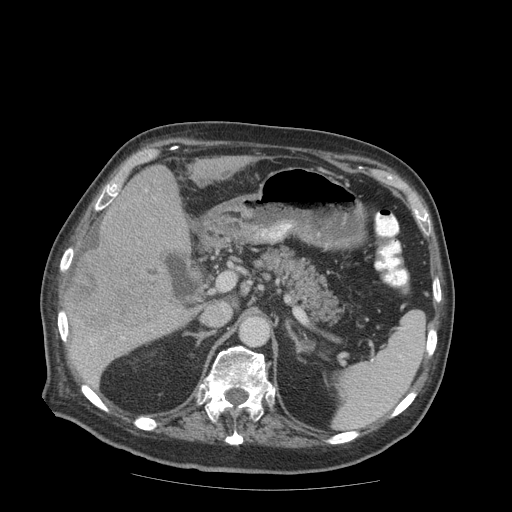
Contrast-enhanced abdominal CT (liver protocol), one axial slice. Position 46 of 99 along the scan axis. Reconstruction kernel STANDARD. 140 kVp. Soft-tissue window (W 400 / L 40 HU). 2.5 mm slice thickness. 512 × 512 image matrix, field of view 420 × 420 mm. From the clinical record (not read from this slice): diagnosis: hepatocellular carcinoma (patient treated with transarterial chemoembolisation; whether this scan precedes or follows treatment is not stated here); TNM stage (as recorded): Stage-IIIB; Child-Pugh class: A; tumour differentiation: well differentiated; tumour nodularity: multinodular.
Structures marked on this image (semi-automatically segmented with operator editing):
- liver parenchyma outside the tumour (the mass and vessels are separate outlines, so this box may not span the whole liver): bounding box <64,164,246,386> (left, top, right, bottom; pixels)
- mass: <65,196,187,332>
- liver vessels: <90,201,124,342>